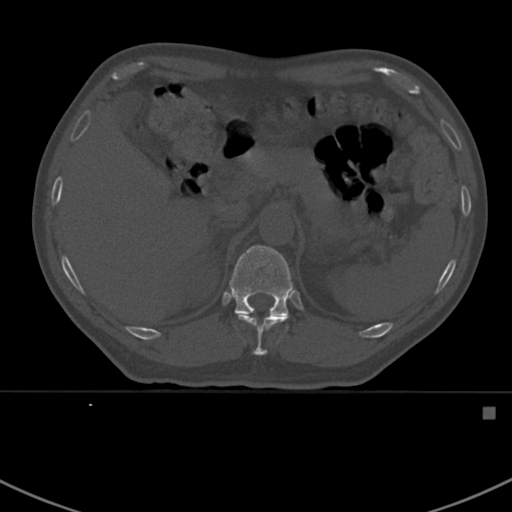
CT including the spine, one axial slice. Slice 337 of 412 in the series (ordered by position). 120 kVp. Bone window (W 1800 / L 400 HU). 1.5 mm slice thickness. 512 × 512 image matrix, field of view 358 × 358 mm. Patient: male, 59 years. Case-level facts recorded for this patient, not image findings: primary cancer: prostate.
Structures marked on this image (semi-automatically segmented with operator editing):
- T11 vertebra: bounding box <237,315,286,356> (left, top, right, bottom; pixels)
- T12 vertebra: <229,245,293,330>